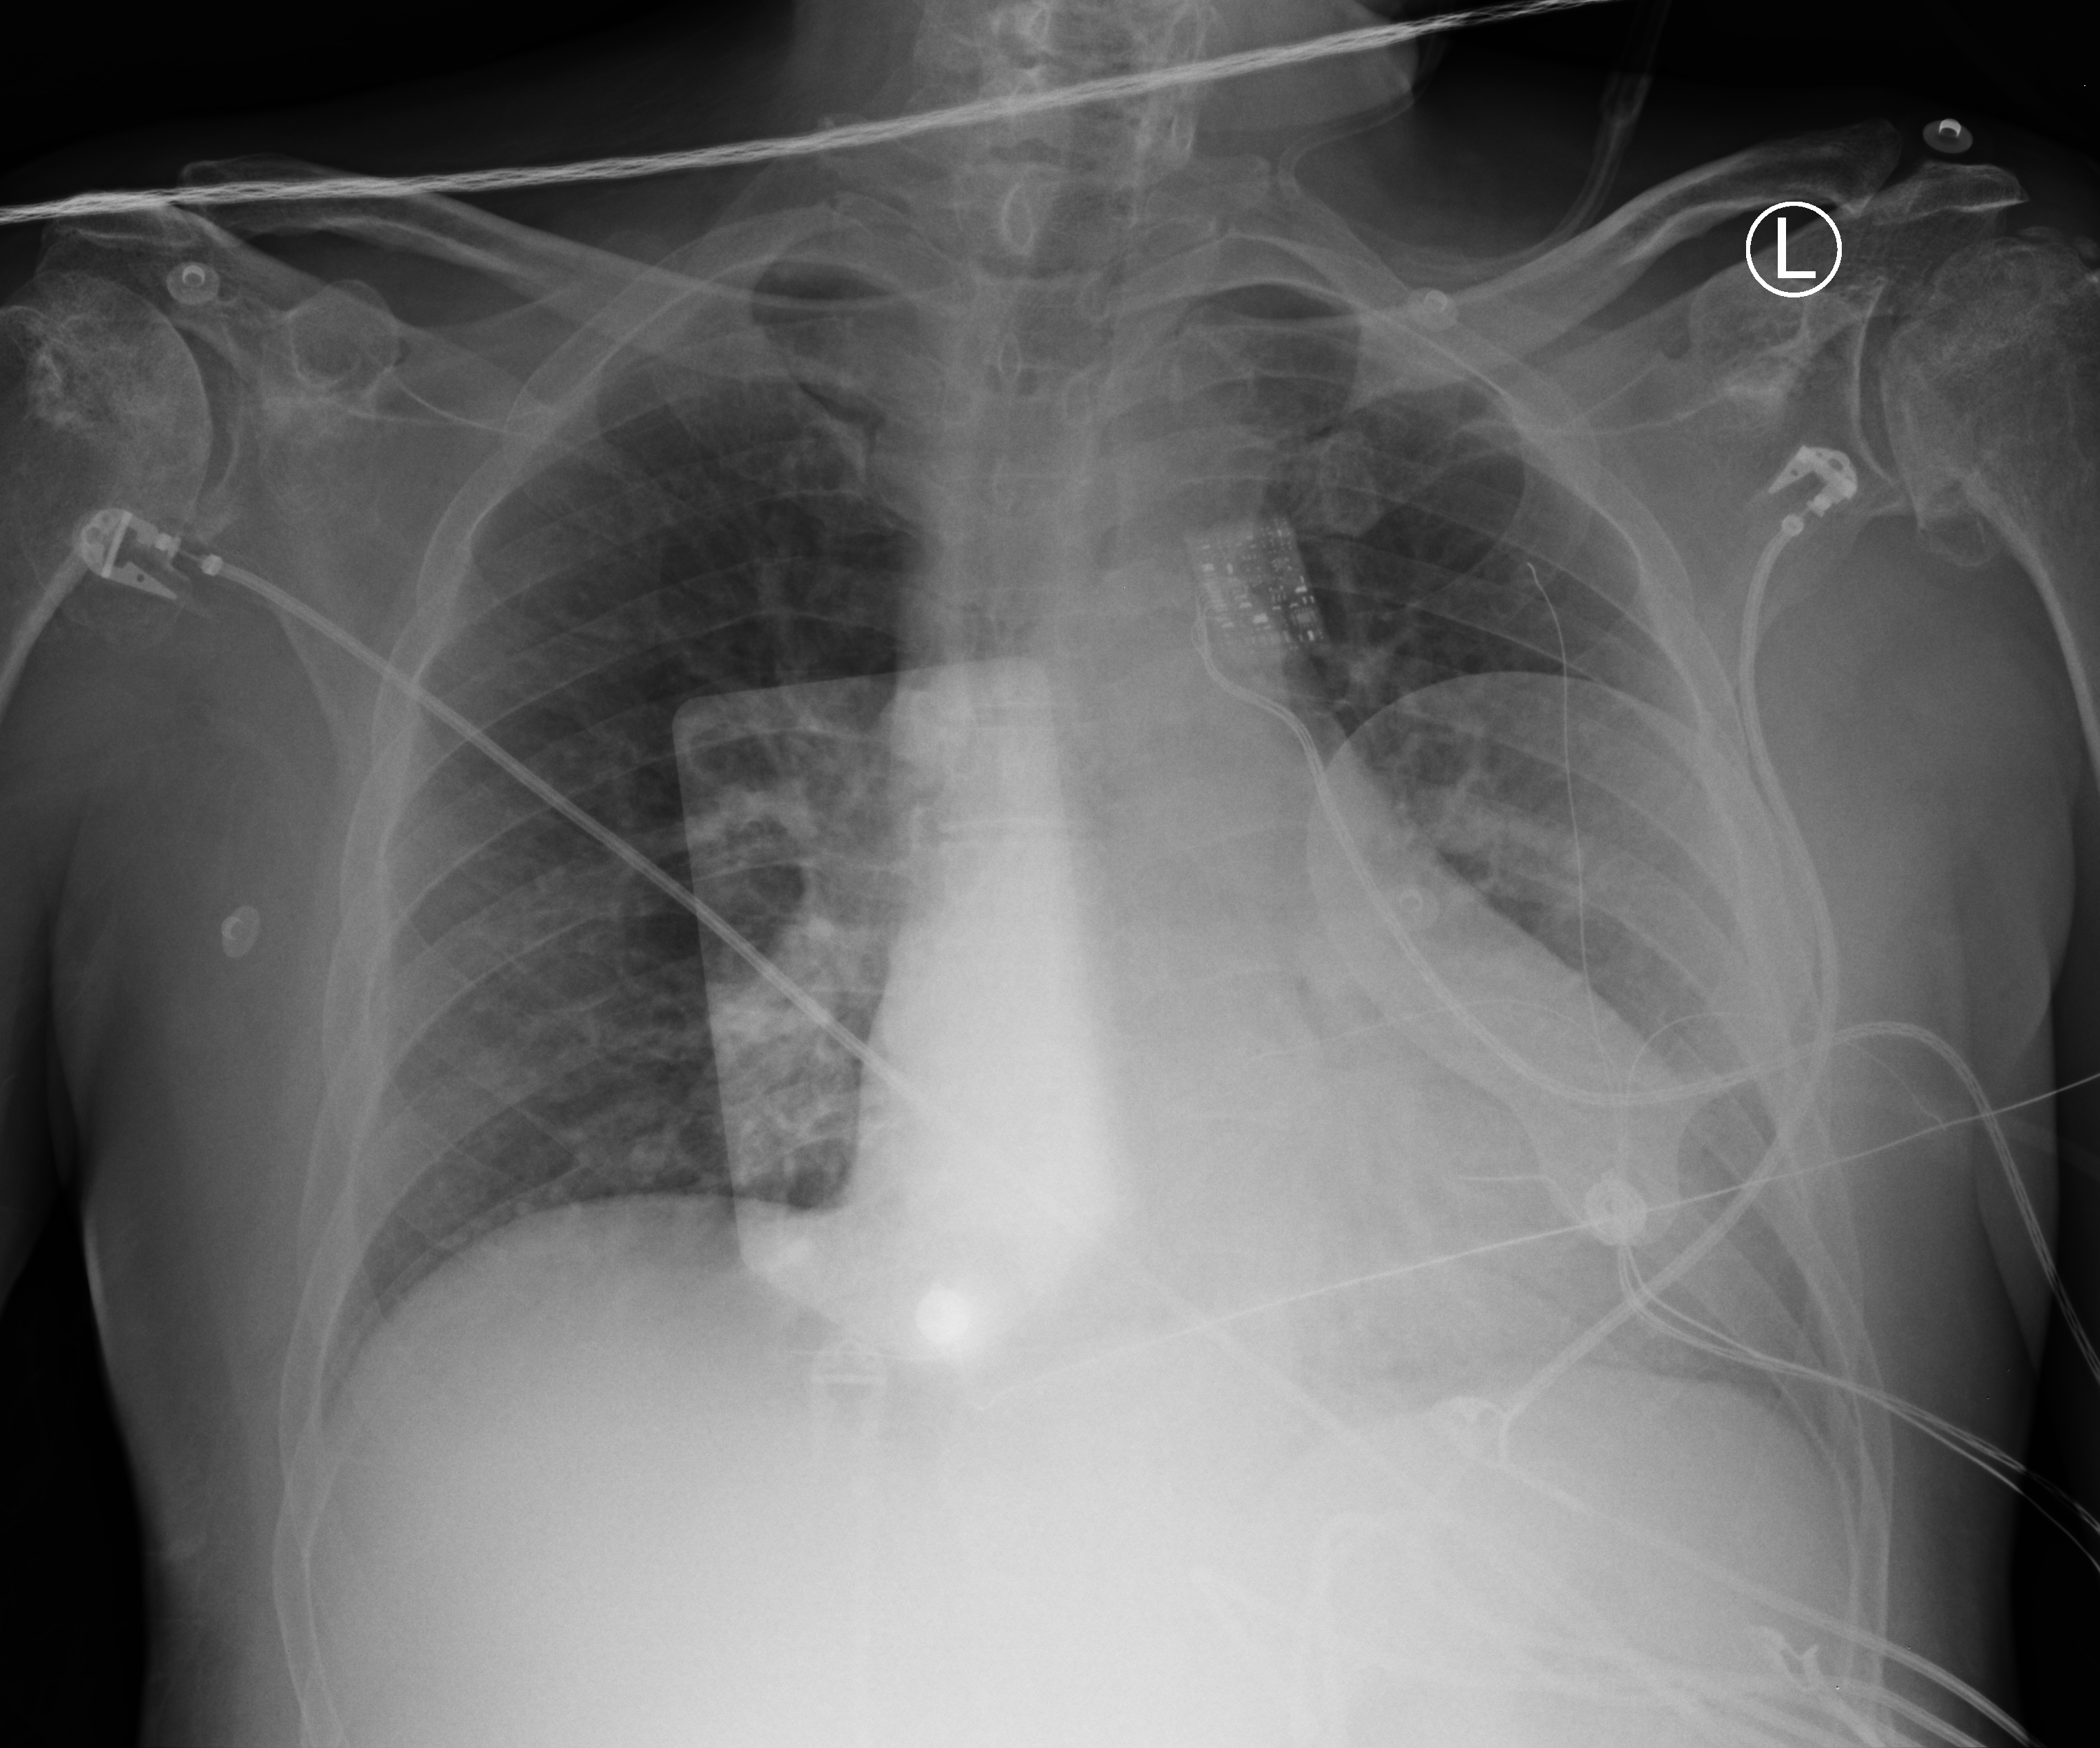
Portable chest radiograph. Male patient hospitalised with COVID-19, age 60–74 years.
Hospital-stay facts (about this admission, not read from this image; timing relative to this image not recorded): mechanically ventilated during this hospital stay: no; diabetes (admission record): yes.